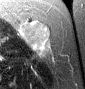
MRI of an extremity soft-tissue mass, one axial slice; slice 26 of 46 in the series (ordered by position); T2-weighted fat-saturated; MR volume resampled by the dataset authors to the PET/CT grid (not the native acquisition matrix); 3.27 mm slice thickness; 85 × 89 image matrix, field of view 83 × 87 mm. Female patient. Case-level facts recorded for this patient, not image findings: histological type: leiomyosarcoma; grade: intermediate; site of the primary tumour: parascapusular.
Structures marked on this image (expert contour drawn on MRI and transferred to this co-registered scan by the dataset authors):
- gross tumour volume including surrounding oedema: bounding box [x1, y1, x2, y2] px = [18, 18, 51, 56]
- gross tumour volume (mass): [22, 18, 51, 47]